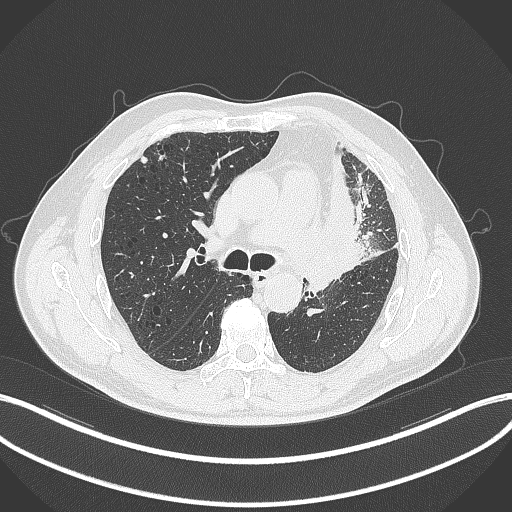
Chest CT, one axial slice; slice 189 of 297 in the series (ordered by position); reconstruction kernel B70f; lung window (W 1500 / L -600 HU); 1 mm slice thickness; 512 × 512 image matrix, field of view 400 × 400 mm. Patient: male, 68 years. From the clinical record (not read from this slice): clinical TNM (as recorded): T3 N3 M1.
Outlined on this slice (bounding box drawn by a radiologist):
- lung tumour (recorded histology: adenocarcinoma): box from (x=323, y=148) to (x=391, y=286) px